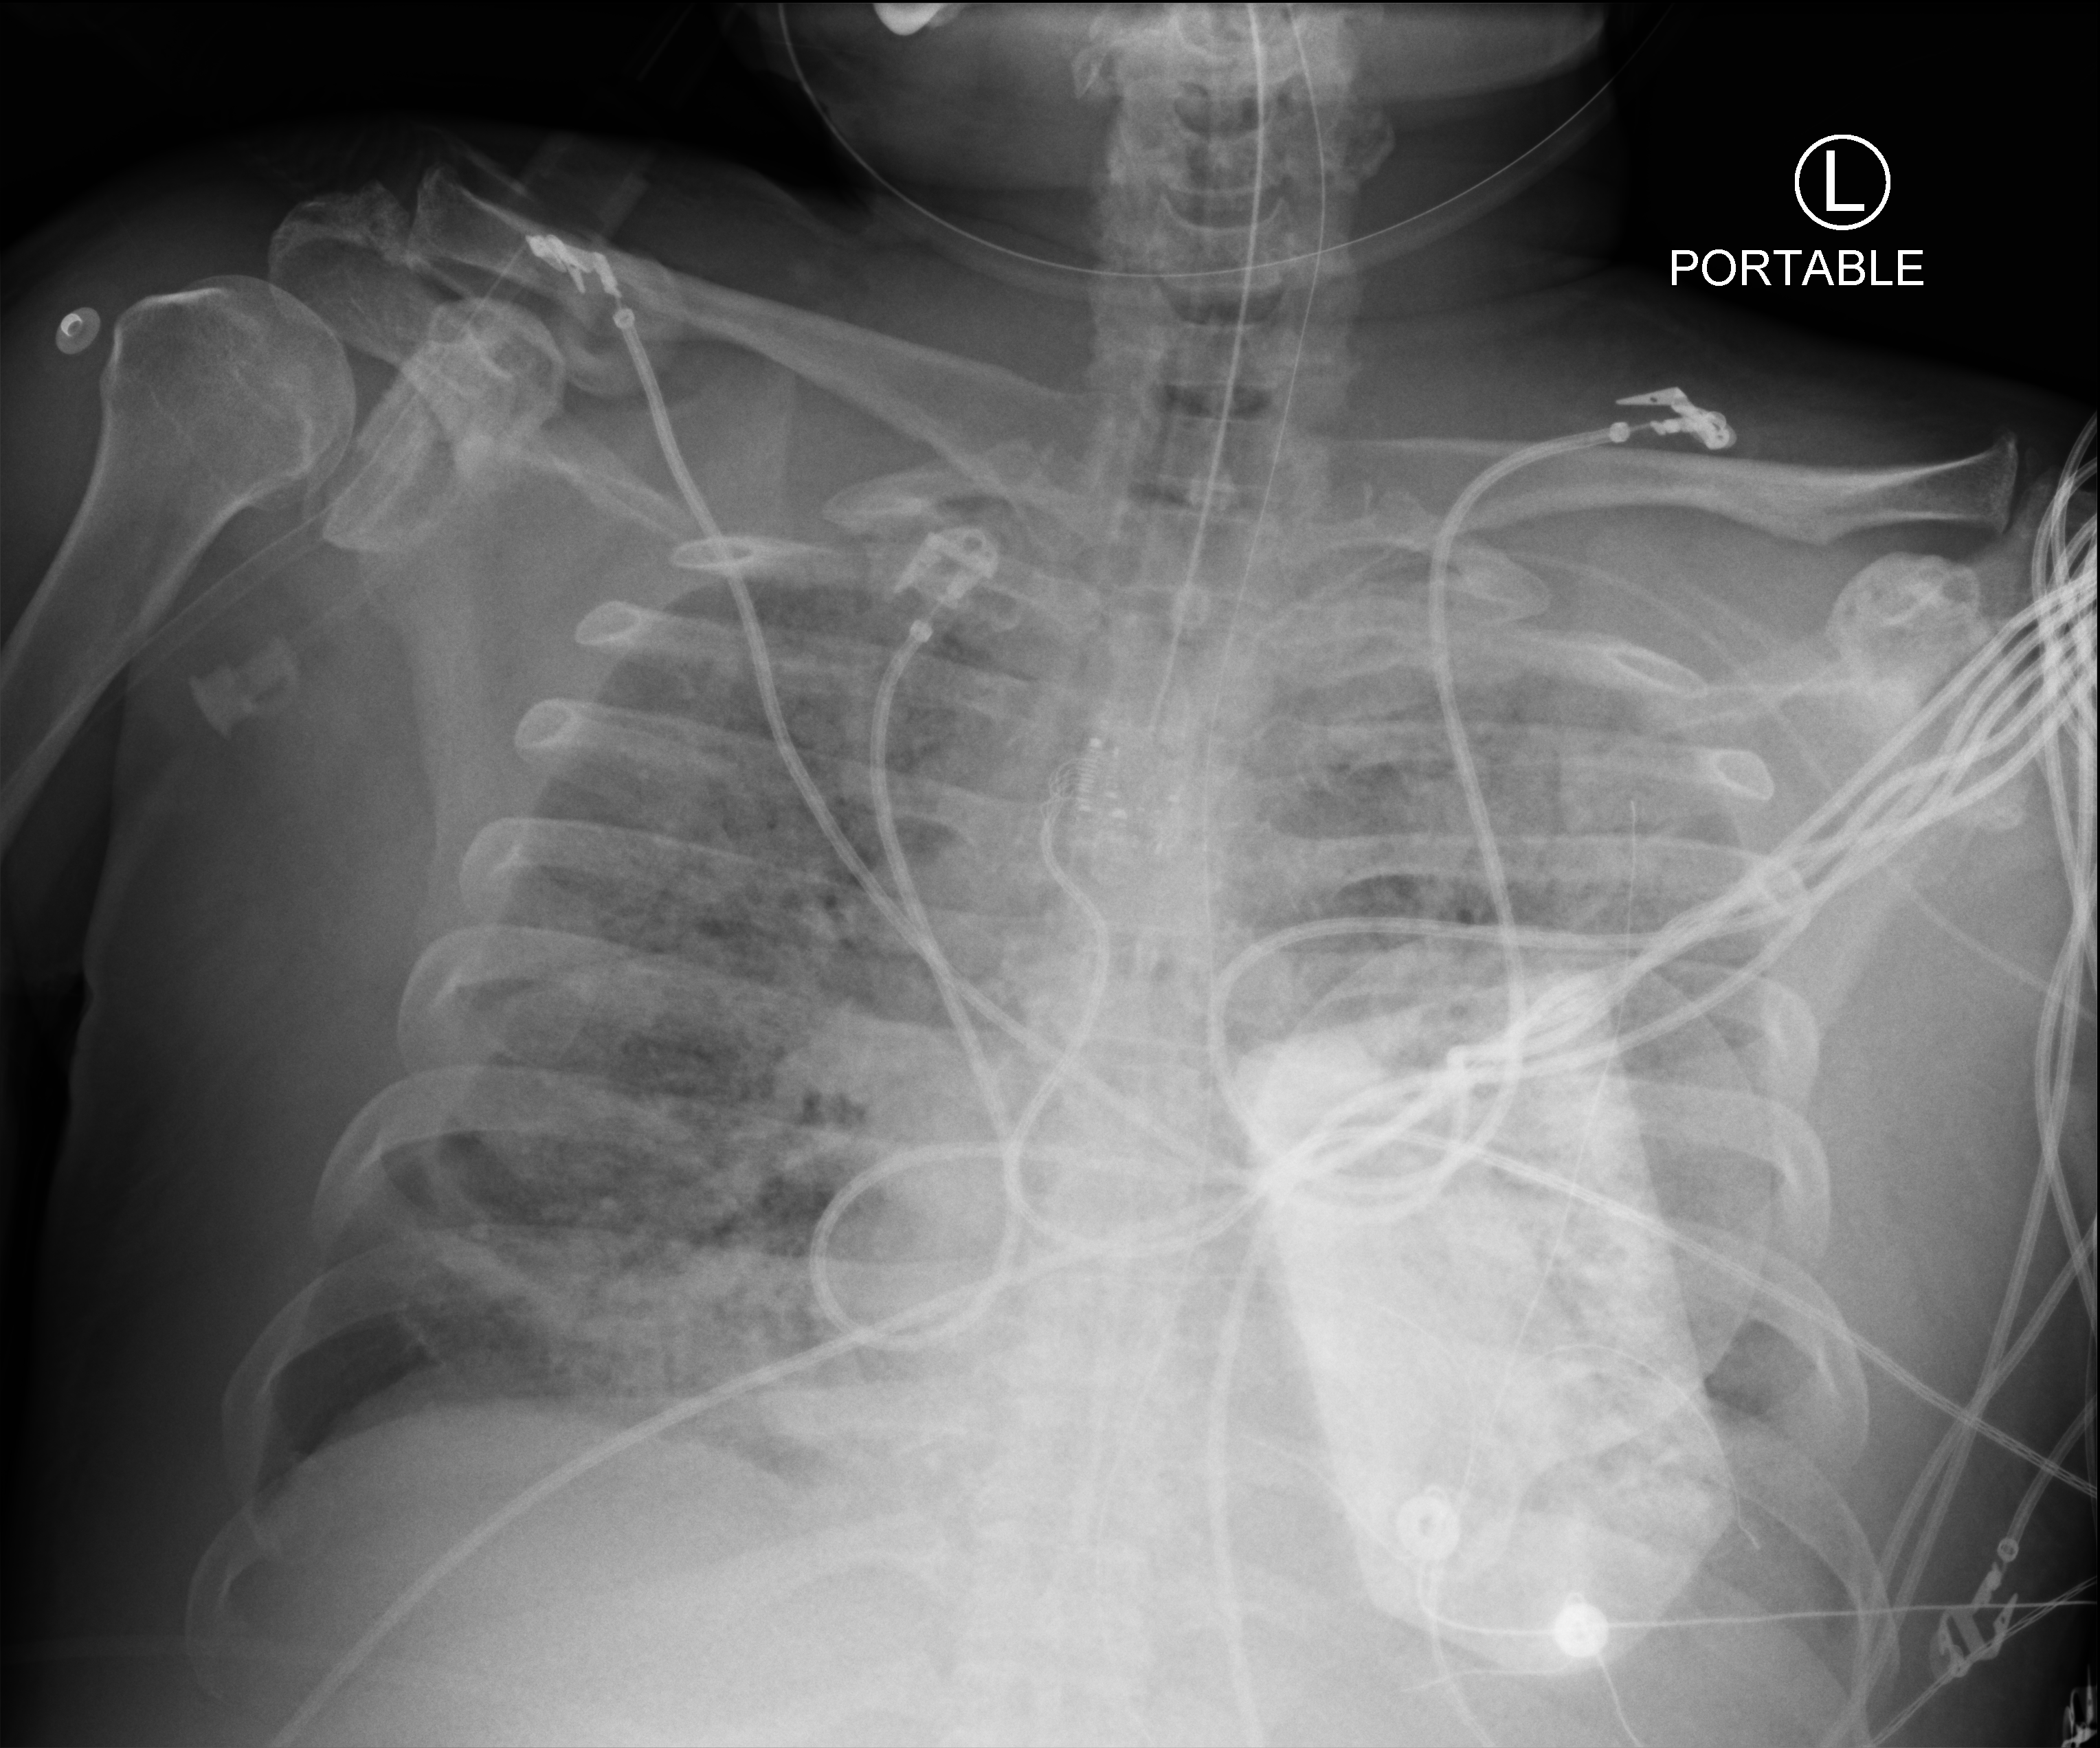
Bedside chest radiograph (computed radiography), anteroposterior (AP) projection. Patient hospitalised with COVID-19; male, aged 60–74 years.
Admission-level facts for this patient (not findings on this image; timing relative to this image not recorded): chronic kidney disease (admission record): no; mechanically ventilated during this hospital stay: yes.